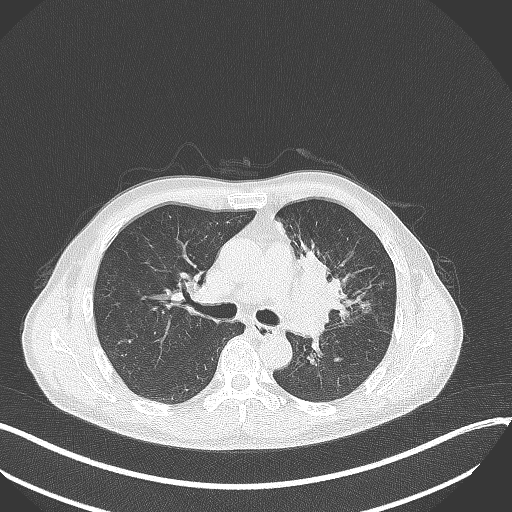
Chest CT, one axial slice. Slice 206 of 411 in the series (ordered by position). Lung window (W 1500 / L -600 HU). 1 mm slice thickness. 512 × 512 image matrix, field of view 400 × 400 mm. Patient: male, 56 years. Case-level facts recorded for this patient, not image findings: clinical TNM (as recorded): T2a N0 M0.
Structures marked on this image (rectangle marked by the reading radiologist):
- lung tumour (recorded histology: squamous cell carcinoma): box from (x=289, y=245) to (x=356, y=331) px